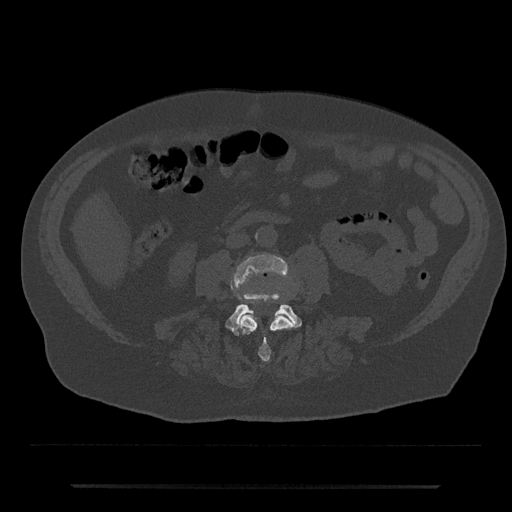
CT including the spine, one axial slice. Position 379 of 797 along the scan axis. 120 kVp. Bone window (W 1800 / L 400 HU). 512 × 512 image matrix. Male patient, age 80 years. From the clinical record (not read from this slice): primary cancer: prostate; vertebrae with lytic lesions (as recorded): L1, T11.
Annotated regions visible in this slice (semi-automatically segmented with operator editing):
- L3 vertebra: bounding box [x1, y1, x2, y2] px = [231, 254, 293, 361]
- L4 vertebra: [225, 294, 302, 335]